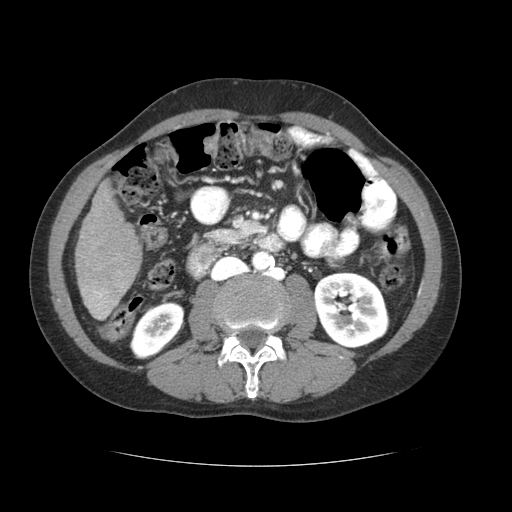
Contrast-enhanced abdominal CT (liver protocol), one axial slice. Position 16 of 69 along the scan axis. Reconstruction kernel STANDARD. 120 kVp. Soft-tissue window (W 400 / L 40 HU). 2.5 mm slice thickness. 512 × 512 image matrix, field of view 360 × 360 mm. Case-level facts recorded for this patient, not image findings: diagnosis: hepatocellular carcinoma (patient treated with transarterial chemoembolisation; whether this scan precedes or follows treatment is not stated here); TNM stage (as recorded): Stage-II; Child-Pugh class: B; tumour differentiation: poorly differentiated; tumour nodularity: multinodular.
Outlined on this slice (semi-automatically segmented with operator editing):
- liver parenchyma outside the tumour (the mass and vessels are separate outlines, so this box may not span the whole liver): box from (x=76, y=181) to (x=142, y=320) px
- liver vessels: (x=89, y=289)–(x=109, y=319)